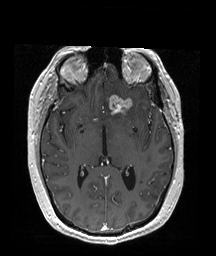
Brain MRI from a brain-tumour surgery series, one axial slice. Slice 101 of 192 in the series (ordered by position). T1-weighted post-contrast. 216 × 256 image matrix, field of view 211 × 250 mm. From the clinical record (not read from this slice): histopathology: Oligodendroglioma; WHO grade: 2; IDH mutation: yes.
Structures marked on this image (outlined manually by an expert reader):
- tumour: bounding box [x1, y1, x2, y2] px = [107, 95, 132, 117]